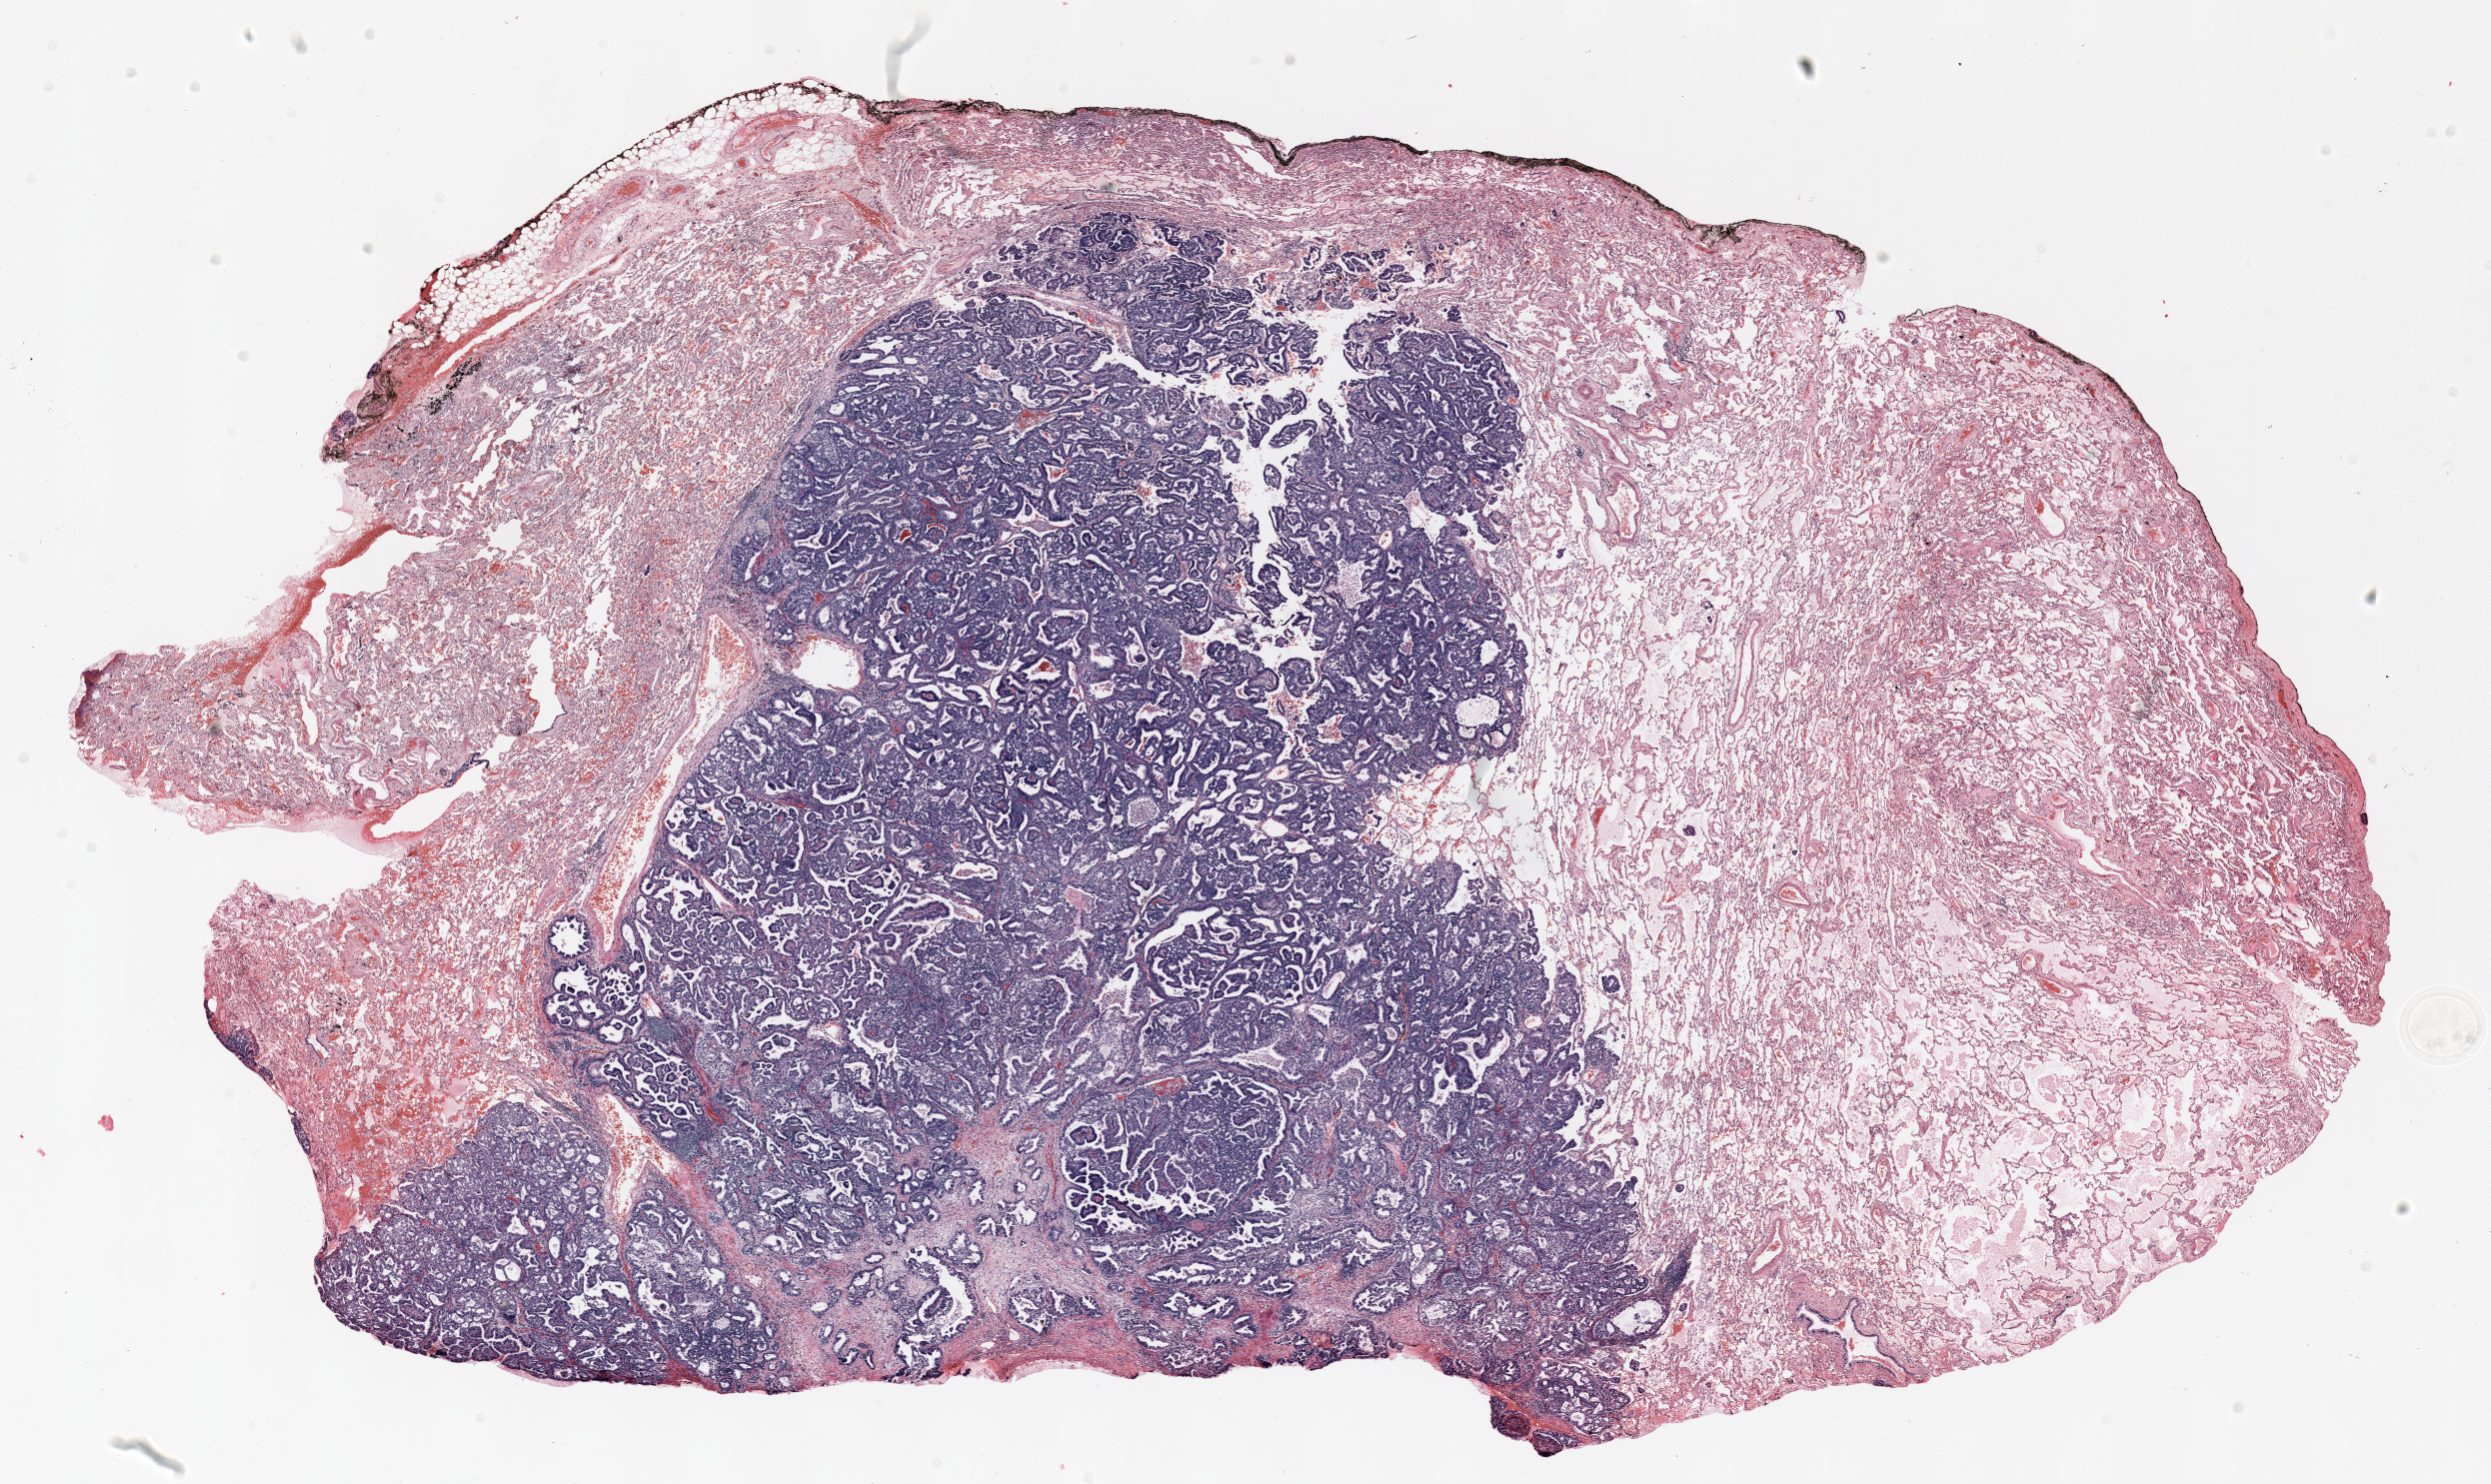
H&E-stained whole-slide image, low-resolution overview of the scanned area, about 20.0 x 11.9 mm; FFPE section; lung tissue. Female, age 67 at enrolment. Former smoker at enrolment. Grade: moderately differentiated (G2).
Participant's lung-cancer diagnosis: Adenocarcinoma, NOS. Stage (AJCC 6th edition): IIA. Primary tumour location (clinical record): left upper lobe. Tumour size (pathology): 23 mm.